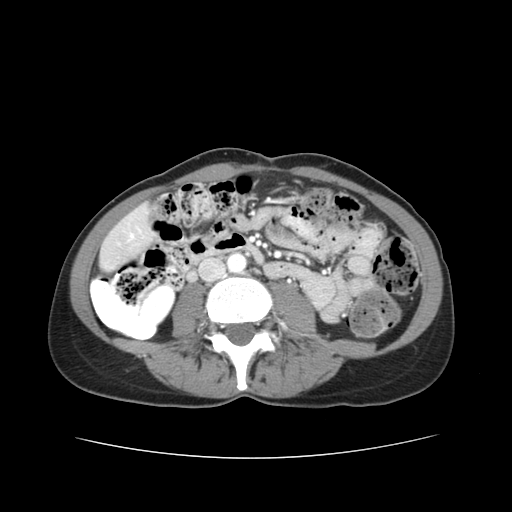
Contrast-enhanced abdominal CT, one axial slice. Slice 6 of 38 in the series (ordered by position). Reconstruction kernel STANDARD. 120 kVp. Intravenous contrast given. Soft-tissue window (W 400 / L 40 HU). 5 mm slice thickness. 512 × 512 image matrix, field of view 340 × 340 mm. Female patient, age 54 years. Case-level facts recorded for this patient, not image findings: diagnosis: colorectal cancer liver metastases, imaged before liver resection; multiple liver metastases: yes; largest metastasis: 1.1 cm; disease in both lobes: yes.
Annotated regions visible in this slice (manually delineated by an expert):
- liver: box from (x=102, y=209) to (x=151, y=264) px